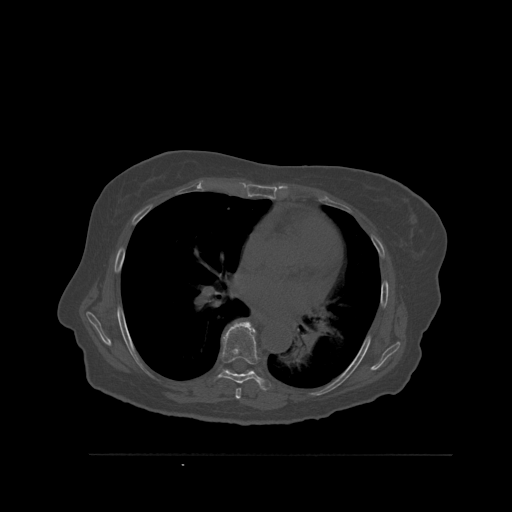
CT including the spine, one axial slice. Position 365 of 527 along the scan axis. Bone window (W 1800 / L 400 HU). 1.5 mm slice thickness. 512 × 512 image matrix, field of view 470 × 470 mm. Patient: female, 73 years. Case-level facts recorded for this patient, not image findings: primary cancer: breast; vertebrae with lytic lesions (as recorded): L2.
Structures marked on this image (semi-automatic segmentation, software-assisted and operator-edited):
- T6 vertebra: bounding box (x1, y1, x2, y2) in pixels: (235, 388, 241, 399)
- T7 vertebra: (207, 321, 271, 391)